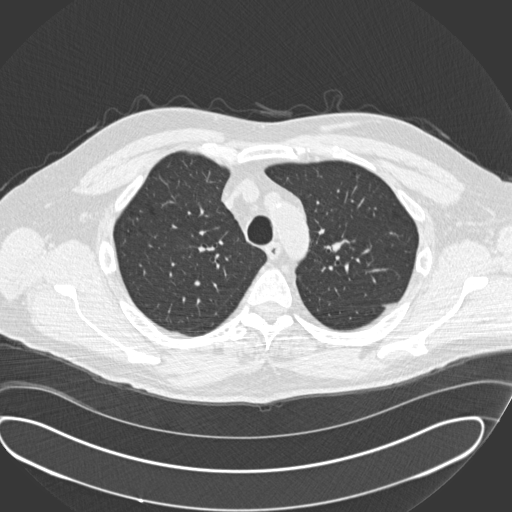
Axial slice from a low-dose chest CT screening exam. Second screening round (one year after baseline). Lung window (W 1500 / L -600 HU). 2 mm slice thickness. 120 kVp. Male, age 56 years at enrolment. Current smoker at enrolment.
Expert reader's lesion annotation, bounding box [x1, y1, x2, y2] px = [311, 224, 368, 271]. No non-calcified nodule or mass ≥4 mm was recorded by the screening reader at this exam. Official screen result: negative screen, significant abnormalities not suspicious for lung cancer. Participant outcome: lung cancer diagnosed 520 days after this screen (after the third annual screen) — neuroendocrine carcinoma, NOS, left upper lobe, well differentiated (G1), stage IA (AJCC 6th edition), 20 mm at pathology.